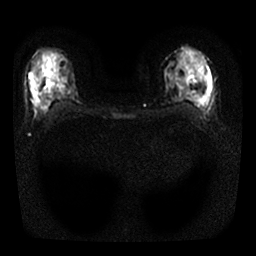
Breast MRI, one axial slice; position 13 of 25 along the scan axis; diffusion-weighted series; image 2 of 4 stored at this slice position (different b-values; order by instance number); 1.5 T; 4 mm slice thickness; 256 × 256 image matrix, field of view 300 × 300 mm. Female patient.
Outlined on this slice (manually delineated by an expert):
- tumour on diffusion-weighted imaging: bounding box <31,89,40,105> (left, top, right, bottom; pixels)